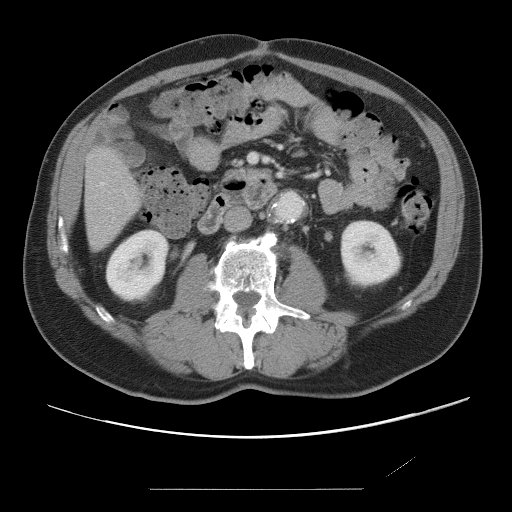
Contrast-enhanced abdominal CT, one axial slice. 120 kVp. Intravenous contrast given. Soft-tissue window (W 400 / L 40 HU). 512 × 512 image matrix, field of view 406 × 406 mm. Male patient, age 74 years. Case-level facts recorded for this patient, not image findings: diagnosis: colorectal cancer liver metastases, imaged before liver resection; multiple liver metastases: yes; largest metastasis: 1.1 cm; disease in both lobes: no.
Outlined on this slice (outlined manually by an expert reader):
- hepatic veins: bounding box (x1, y1, x2, y2) in pixels: (101, 182, 104, 185)
- liver: (86, 149, 140, 250)
- planned liver remnant (the part of the liver to remain after resection): (86, 149, 140, 250)